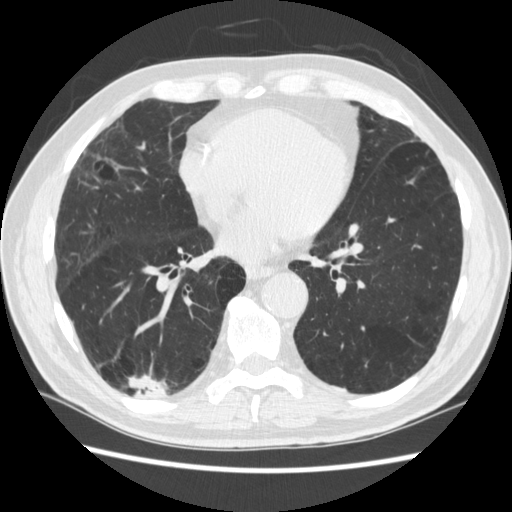
Low-dose screening chest CT, axial slice. Third screening round (two years after baseline). Lung window (W 1500 / L -600 HU). 1.25 mm slice thickness. Male participant, aged 70 years at enrolment. Former smoker at enrolment.
Lesion marked by an expert reader, box from (x=126, y=360) to (x=181, y=417) px. The screening reader recorded 4 non-calcified nodules or masses ≥4 mm on this exam (right lower lobe, right lower lobe, left lower lobe, left lower lobe); which of them this box marks is not recorded. Official screen result: positive, other. Lung cancer was diagnosed 253 days after this screen: squamous cell carcinoma, NOS, right upper lobe, poorly differentiated (G3), stage IV (AJCC 6th edition).